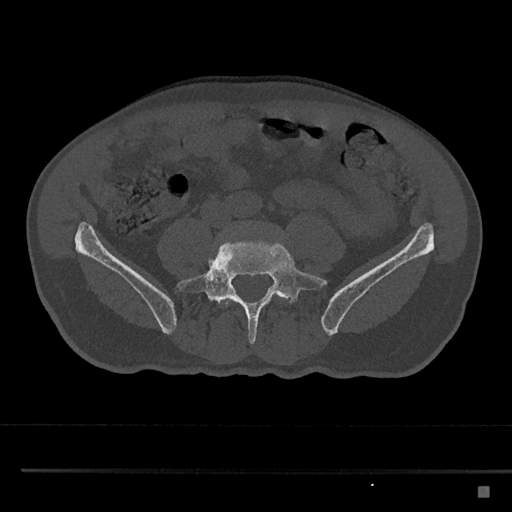
CT including the spine, one axial slice; position 592 of 797 along the scan axis; reconstruction kernel Br40s/3; bone window (W 1800 / L 400 HU); 0.5 mm slice thickness; 512 × 512 image matrix. Patient: male, 59 years. From the clinical record (not read from this slice): primary cancer: prostate.
Structures marked on this image (semi-automatically segmented with operator editing):
- L4 vertebra: bounding box <220,235,227,305> (left, top, right, bottom; pixels)
- L5 vertebra: <177,237,327,345>